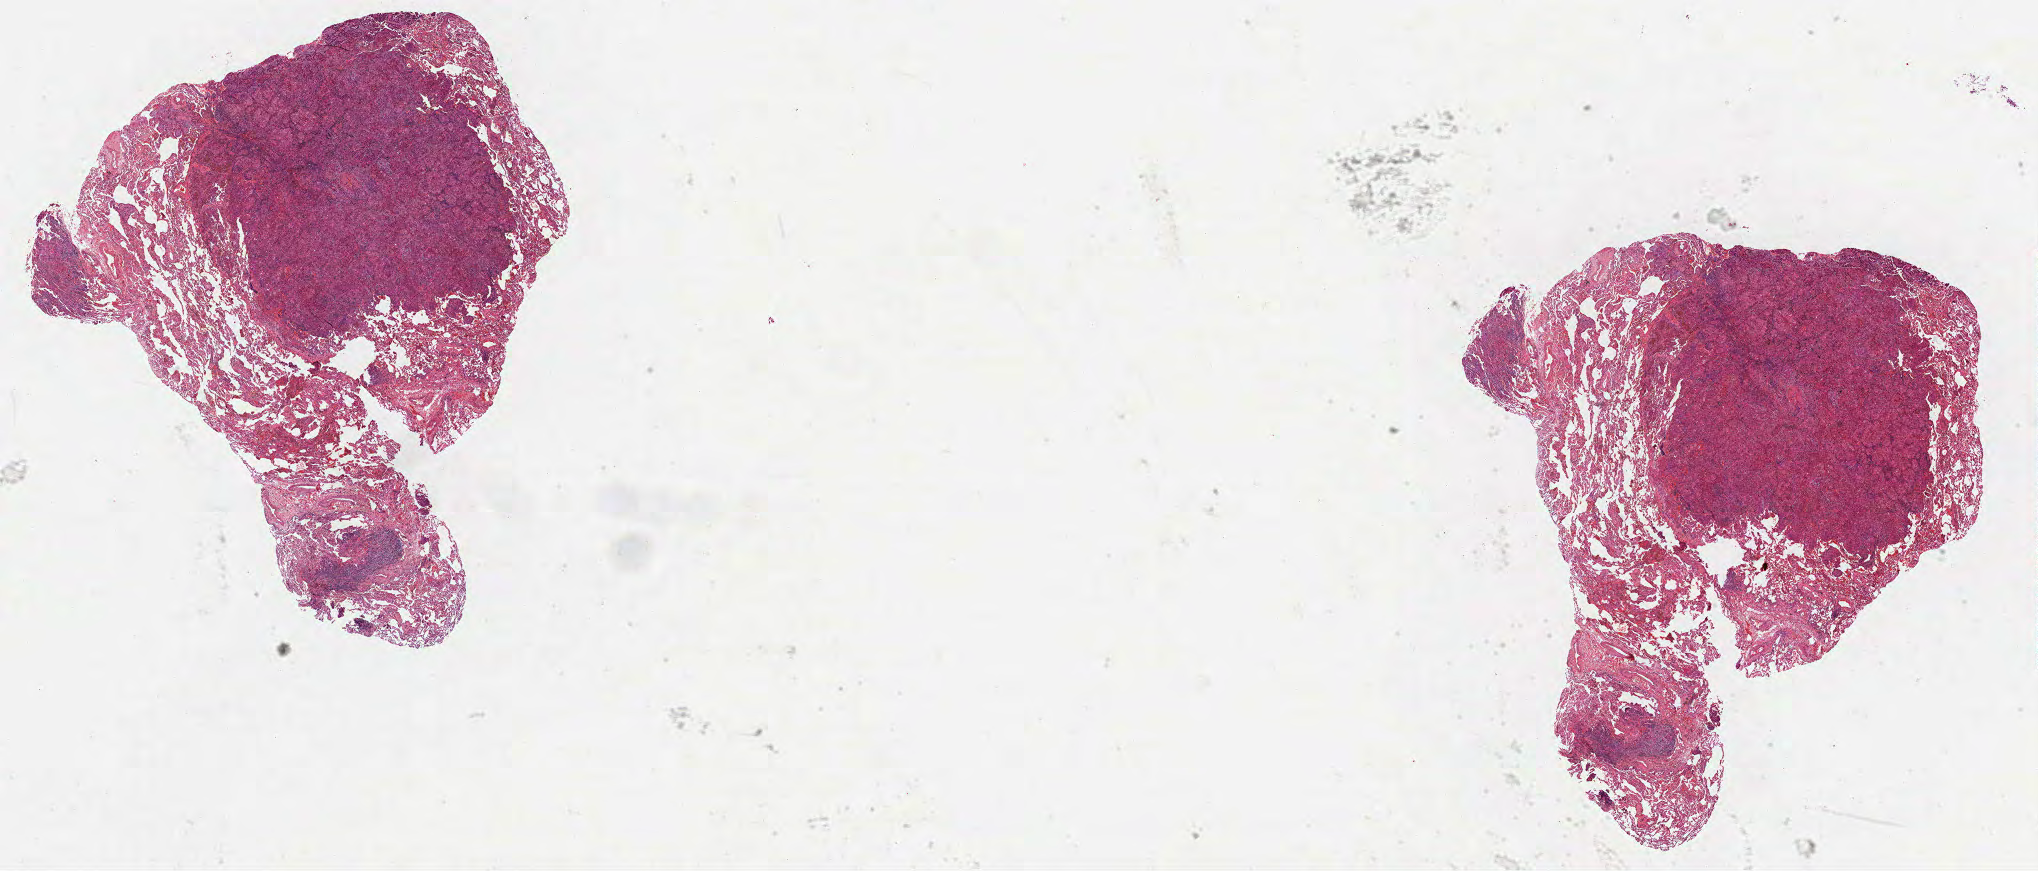
H&E-stained whole-slide image, a low-resolution overview of the entire scanned area, about 32.9 x 14.1 mm; formalin-fixed paraffin-embedded (FFPE) diagnostic section; lung, primary tumour sample. Male patient; age at initial diagnosis 59 years.
• AJCC pathologic stage: IB (6th edition)
• TNM: T2 N0 M0
• laterality: right
• diagnosis: Adenocarcinoma, NOS (upper lobe, lung)